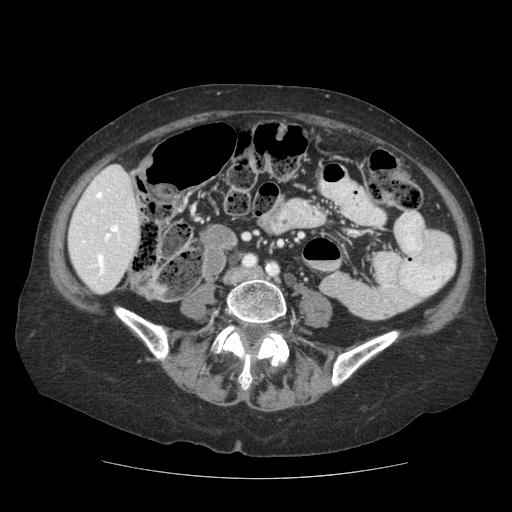
Contrast-enhanced abdominal CT (liver protocol), one axial slice; position 29 of 111 along the scan axis; reconstruction kernel STANDARD; soft-tissue window (W 400 / L 40 HU); 2.5 mm slice thickness; 512 × 512 image matrix, field of view 360 × 360 mm. Case-level facts recorded for this patient, not image findings: diagnosis: hepatocellular carcinoma (patient treated with transarterial chemoembolisation; whether this scan precedes or follows treatment is not stated here); TNM stage (as recorded): Stage-I; Child-Pugh class: A; tumour differentiation: moderately-poorly differentiated; tumour nodularity: uninodular.
Outlined on this slice (semi-automatic segmentation, software-assisted and operator-edited):
- liver parenchyma outside the tumour (the mass and vessels are separate outlines, so this box may not span the whole liver): bounding box <68,165,140,294> (left, top, right, bottom; pixels)
- liver vessels: <81,190,120,276>